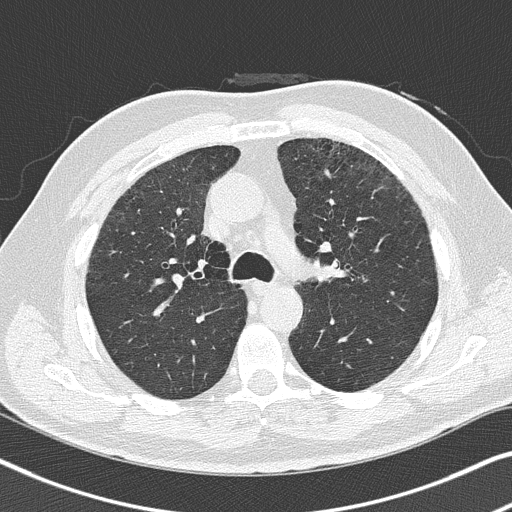
Axial slice from a low-dose chest CT screening exam. Baseline annual screen. Lung window (W 1500 / L -600 HU). 2 mm slice thickness. Slice 108 of 300 in the series. 512 × 512 image matrix. Male participant, aged 64 years at enrolment. Current smoker at enrolment.
- Lesion marked by an expert reader, box from (x=322, y=249) to (x=355, y=278) px.
- The exam's reader record, not a measurement of the box and not confirmed to be the same lesion: non-calcified nodule or mass ≥4 mm, left upper lobe, 4 × 4 mm, smooth margins, soft tissue attenuation.
- Official screen result: positive, change unspecified: nodule(s) >= 4 mm or enlarging nodule(s), mass(es), or other non-specific abnormalities suspicious for lung cancer.
- Participant outcome: lung cancer diagnosed 450 days after this screen (after the second annual screen) — squamous cell carcinoma, keratinizing, NOS, left upper lobe, moderately differentiated (G2), stage IA (AJCC 6th edition), 4 mm at pathology.